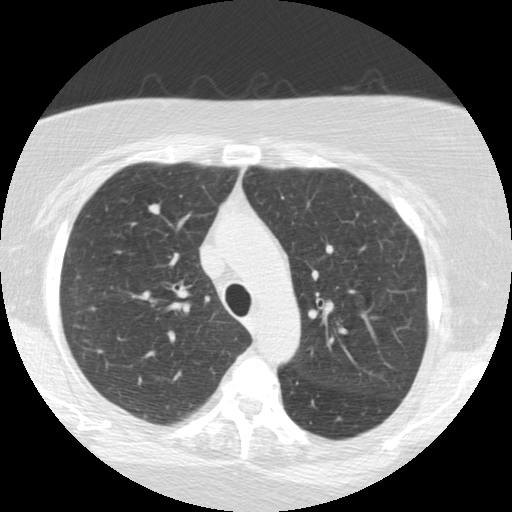
Low-dose screening chest CT, axial slice; second annual screen; lung window (W 1500 / L -600 HU); standard (soft-tissue) reconstruction kernel (STANDARD); 120 kVp; slice 169 of 225 in the series; 512 × 512 image matrix, field of view 320 × 320 mm. Female participant, aged 64 years at enrolment. Current smoker at enrolment.
Expert reader's lesion annotation, bounding box <130,195,170,232> (left, top, right, bottom; pixels). Screening reader's record for this exam (one nodule recorded; not confirmed to be the boxed lesion): non-calcified nodule or mass ≥4 mm, right upper lobe, 8 × 7 mm, smooth margins, soft tissue attenuation, pre-existing on the prior screen: no. Later outcome: lung cancer diagnosed 85 days after this screen — large cell neuroendocrine carcinoma, right upper lobe, stage IA (AJCC 6th edition), 12 mm at pathology.